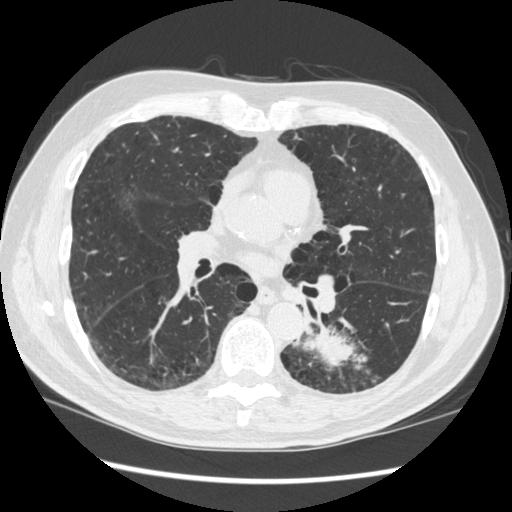
Low-dose screening chest CT, axial slice, baseline annual screen, lung window (W 1500 / L -600 HU), 1.25 mm slice thickness, standard (soft-tissue) reconstruction kernel (STANDARD), slice 166 of 348 in the series. Male, age 72 years at enrolment. Current smoker at enrolment.
Expert reader's lesion annotation, bounding box <264,306,368,399> (left, top, right, bottom; pixels). The screening reader recorded 2 non-calcified nodules or masses ≥4 mm on this exam (left lower lobe, right middle lobe); which of them this box marks is not recorded. Official screen result: positive, change unspecified: nodule(s) >= 4 mm or enlarging nodule(s), mass(es), or other non-specific abnormalities suspicious for lung cancer. Later outcome: lung cancer diagnosed 37 days after this screen — squamous cell carcinoma, NOS, left lower lobe, stage IIIA (AJCC 6th edition), 60 mm at pathology.